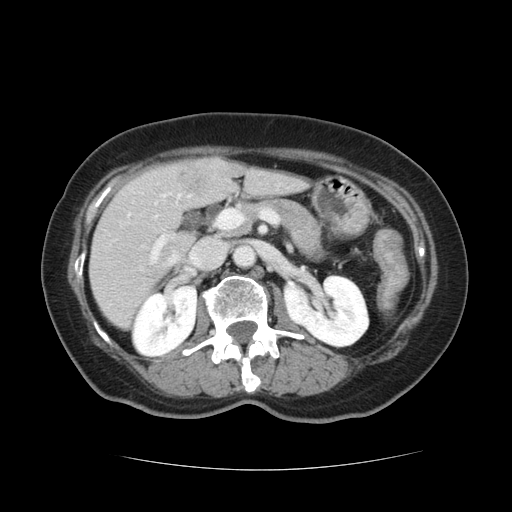
Contrast-enhanced abdominal CT, one axial slice. Slice 56 of 128 in the series (ordered by position). 120 kVp. Soft-tissue window (W 400 / L 40 HU). 512 × 512 image matrix. Female patient, age 67 years. Case-level facts recorded for this patient, not image findings: diagnosis: colorectal cancer liver metastases, imaged before liver resection; multiple liver metastases: yes.
Annotated regions visible in this slice (outlined manually by an expert reader):
- hepatic veins: bounding box (x1, y1, x2, y2) in pixels: (167, 253, 179, 264)
- liver: (91, 159, 305, 328)
- planned liver remnant (the part of the liver to remain after resection): (91, 168, 304, 328)
- portal vein (with intrahepatic branches): (141, 212, 241, 263)
- liver metastasis: (179, 168, 207, 196)